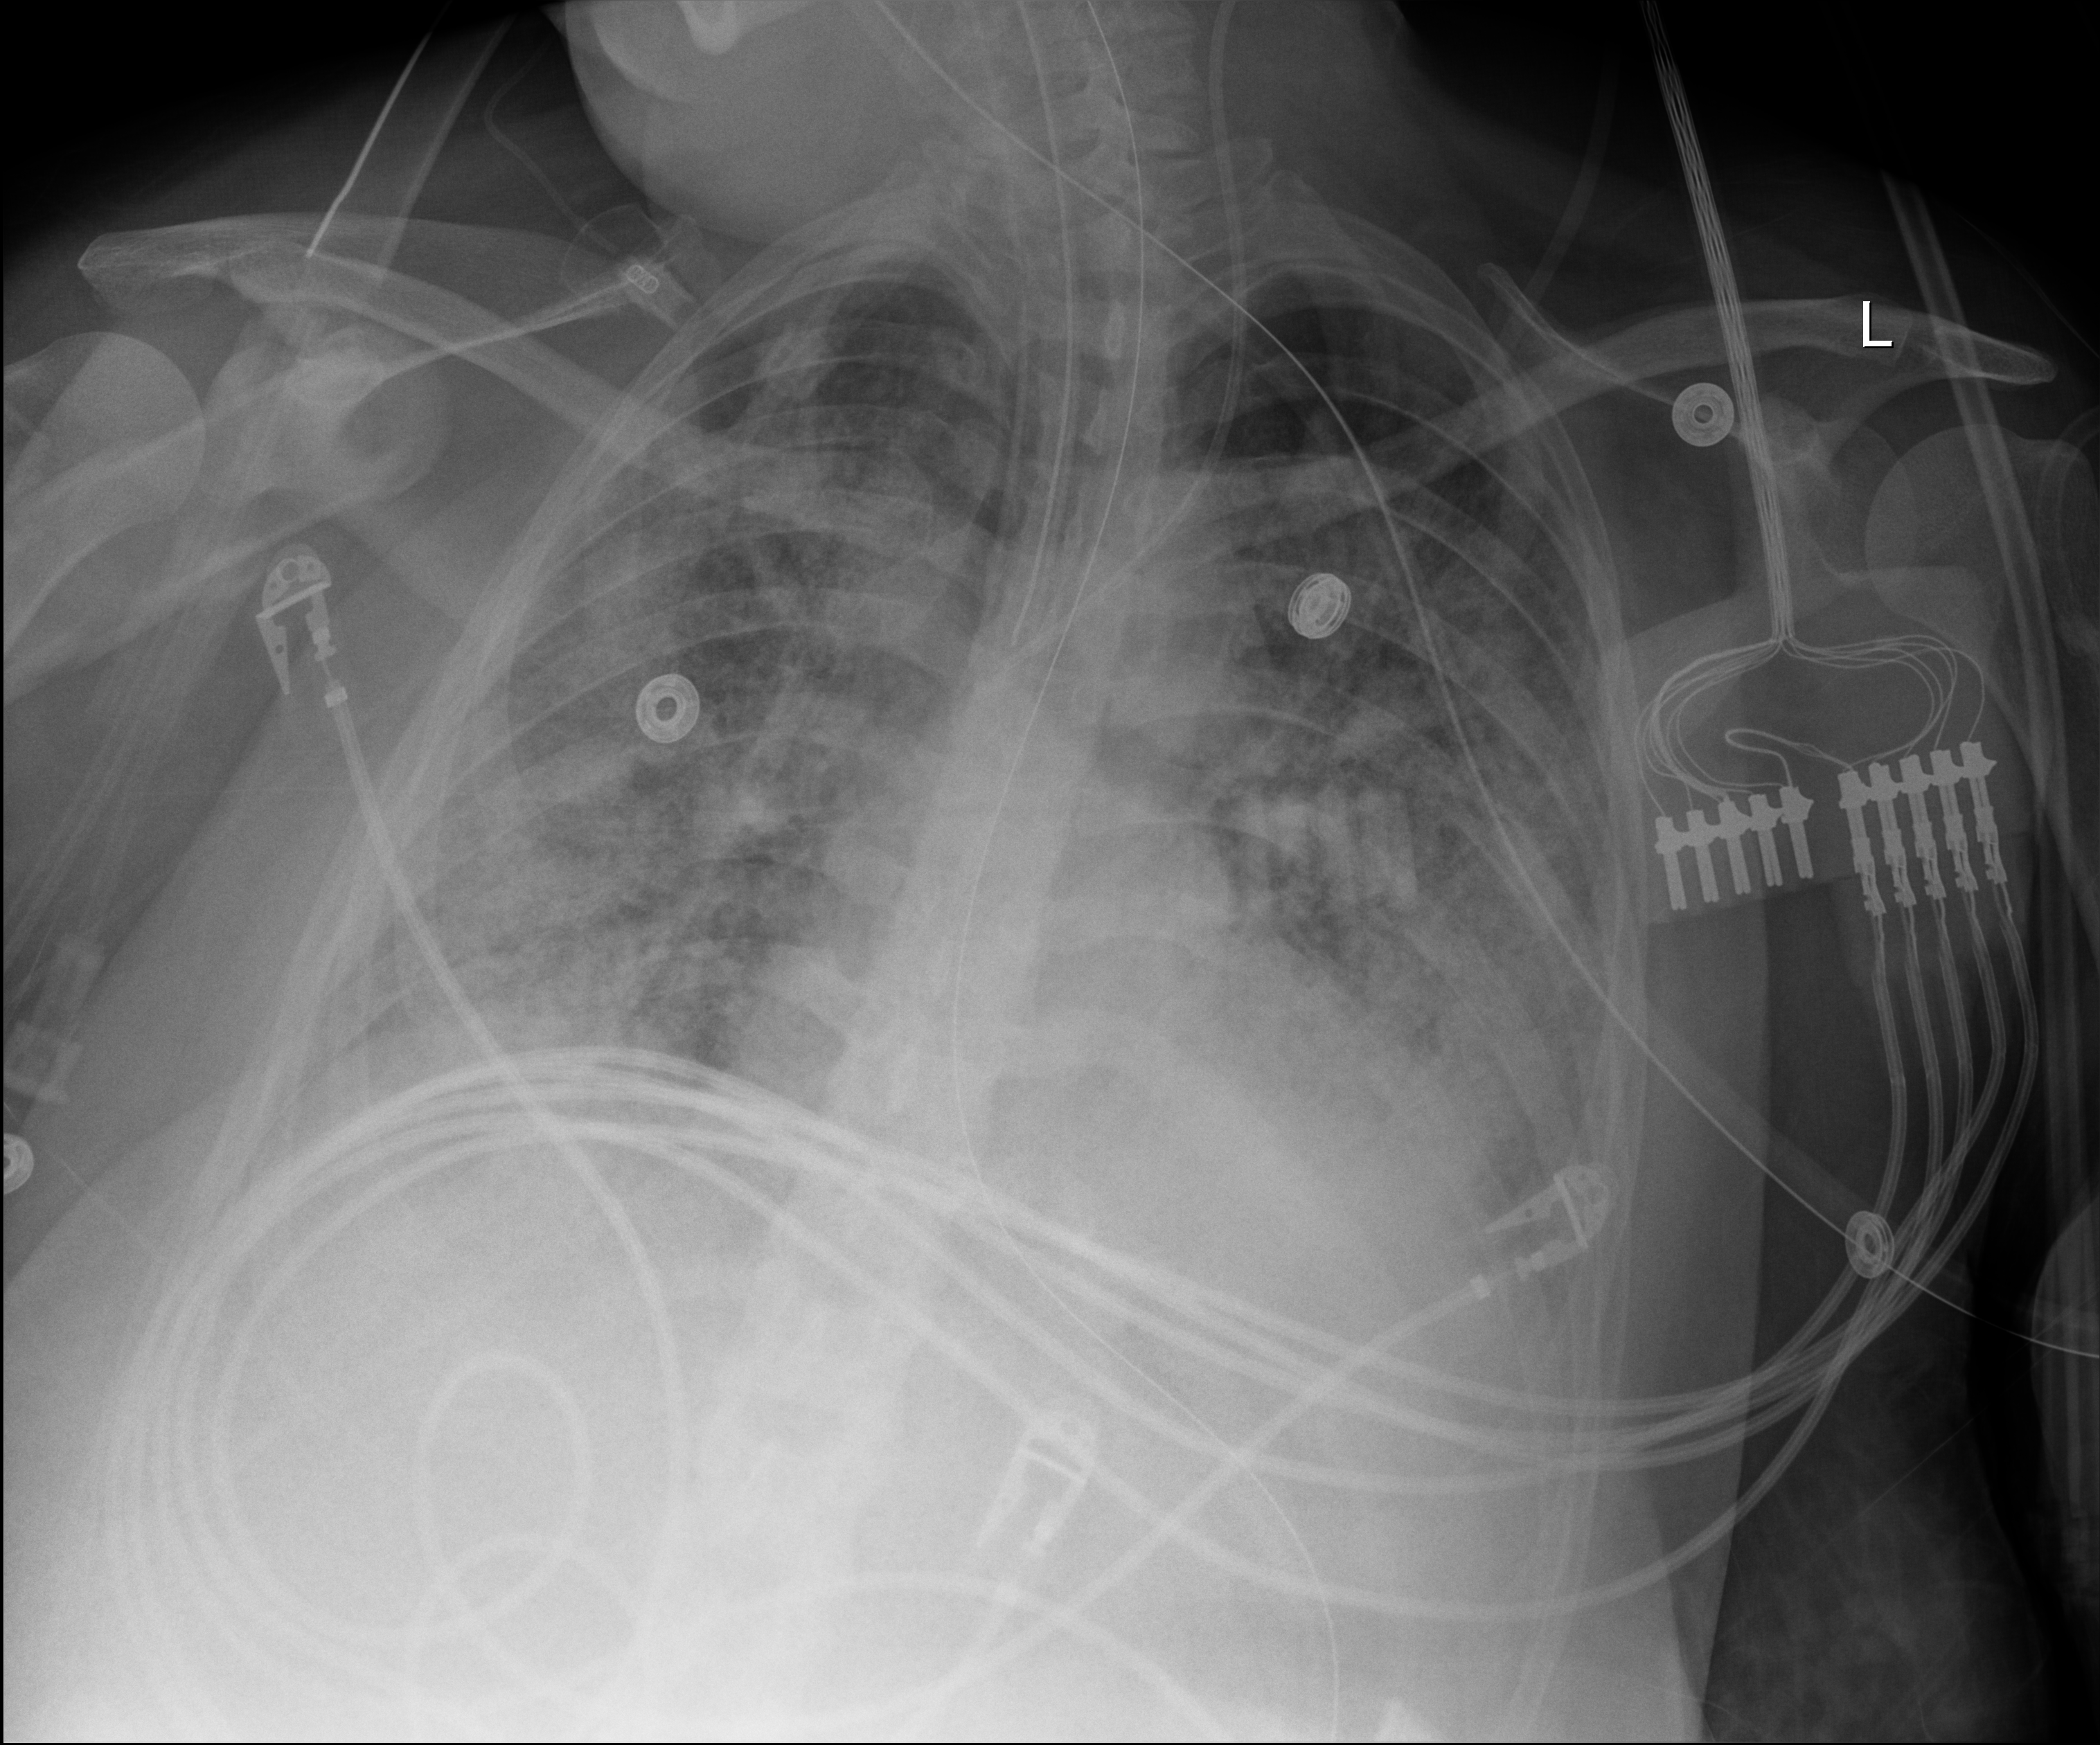
Portable chest radiograph. Patient hospitalised with COVID-19; female, aged 18–59 years.
From the hospital-stay record, not from the radiograph (when in the stay this image was taken is not recorded):
- length of hospital stay: 33 days